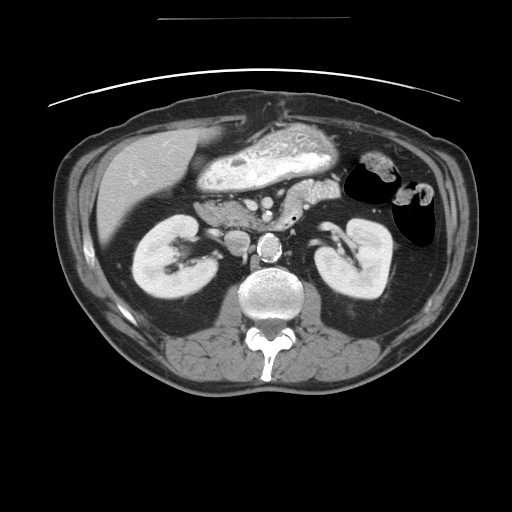
Contrast-enhanced abdominal CT, one axial slice; slice 18 of 49 in the series (ordered by position); reconstruction kernel STANDARD; intravenous contrast given; soft-tissue window (W 400 / L 40 HU); 5 mm slice thickness; 512 × 512 image matrix, field of view 413 × 413 mm. Male patient, age 57 years. Case-level facts recorded for this patient, not image findings: diagnosis: colorectal cancer liver metastases, imaged before liver resection; multiple liver metastases: yes; largest metastasis: 4 cm; disease in both lobes: no.
Outlined on this slice (outlined manually by an expert reader):
- hepatic veins: bounding box (x1, y1, x2, y2) in pixels: (140, 170, 142, 172)
- liver: (97, 127, 218, 244)